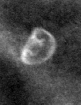
Crop from a digitized film mammogram around one marked abnormality; right breast; CC view.
- Calcifications, morphology lucent center; BI-RADS assessment category 2; subtlety rating 3 on a 1 (subtle) to 5 (obvious) scale; benign; no additional work-up was recommended (benign without callback).